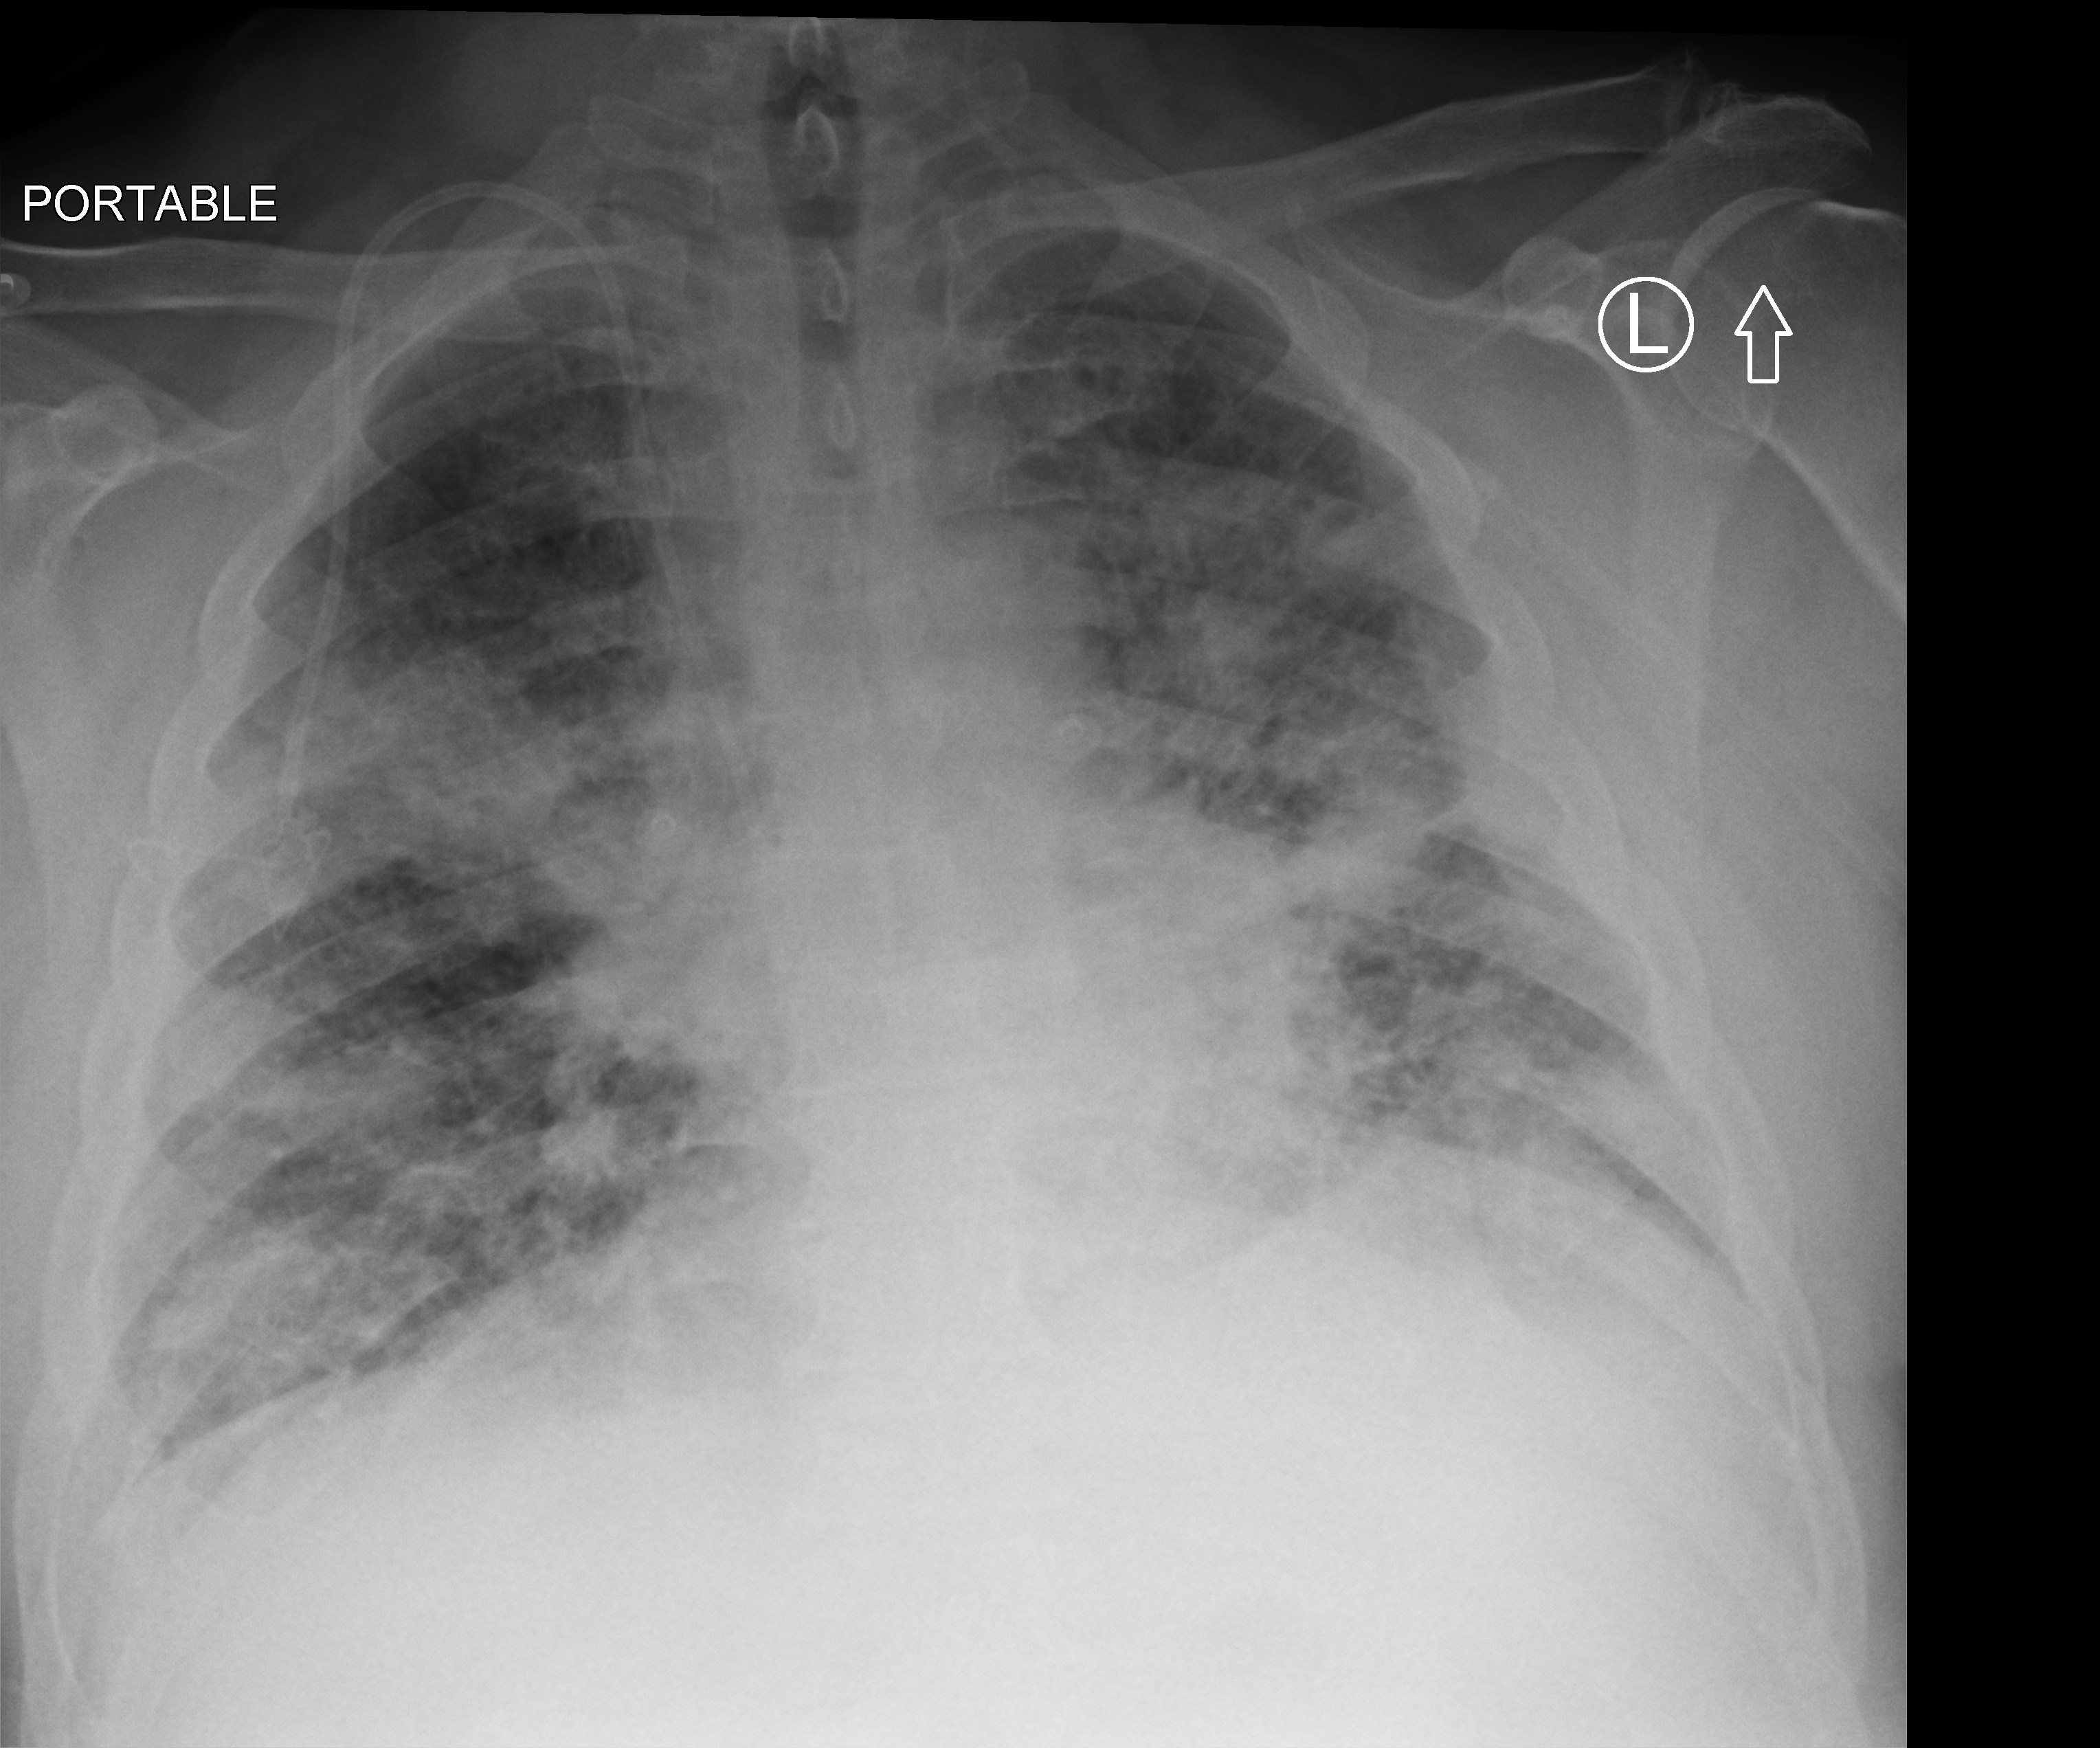
Bedside chest radiograph (computed radiography); anteroposterior (AP) projection. Patient hospitalised with COVID-19; male, aged 60–74 years.
Hospital-stay facts (about this admission, not read from this image; timing relative to this image not recorded):
- admitted to intensive care during this hospital stay: no
- length of hospital stay: 8 days